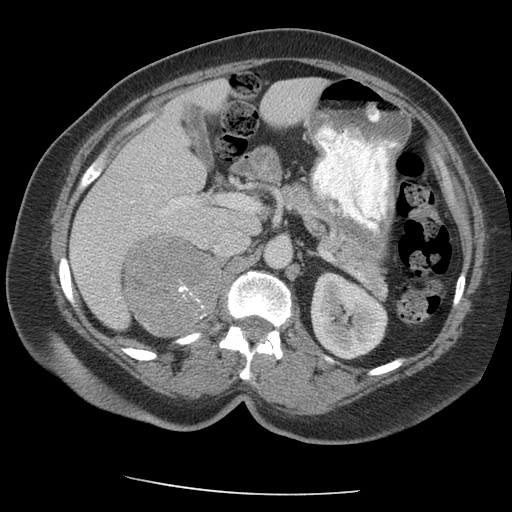
Contrast-enhanced abdominal CT, one axial slice; position 122 of 163 along the scan axis; 140 kVp; intravenous contrast given; soft-tissue window (W 400 / L 40 HU); 2.5 mm slice thickness; 512 × 512 image matrix. Female patient, age 70 years. Case-level facts recorded for this patient, not image findings: diagnosis: adrenocortical carcinoma; tumour side: right adrenal; tumour size at pathology: 9.5 cm; Ki-67 index: 5 %; stage (as recorded): 2.
Structures marked on this image (semi-automatically segmented with operator editing):
- mass: bounding box [x1, y1, x2, y2] px = [126, 238, 218, 333]